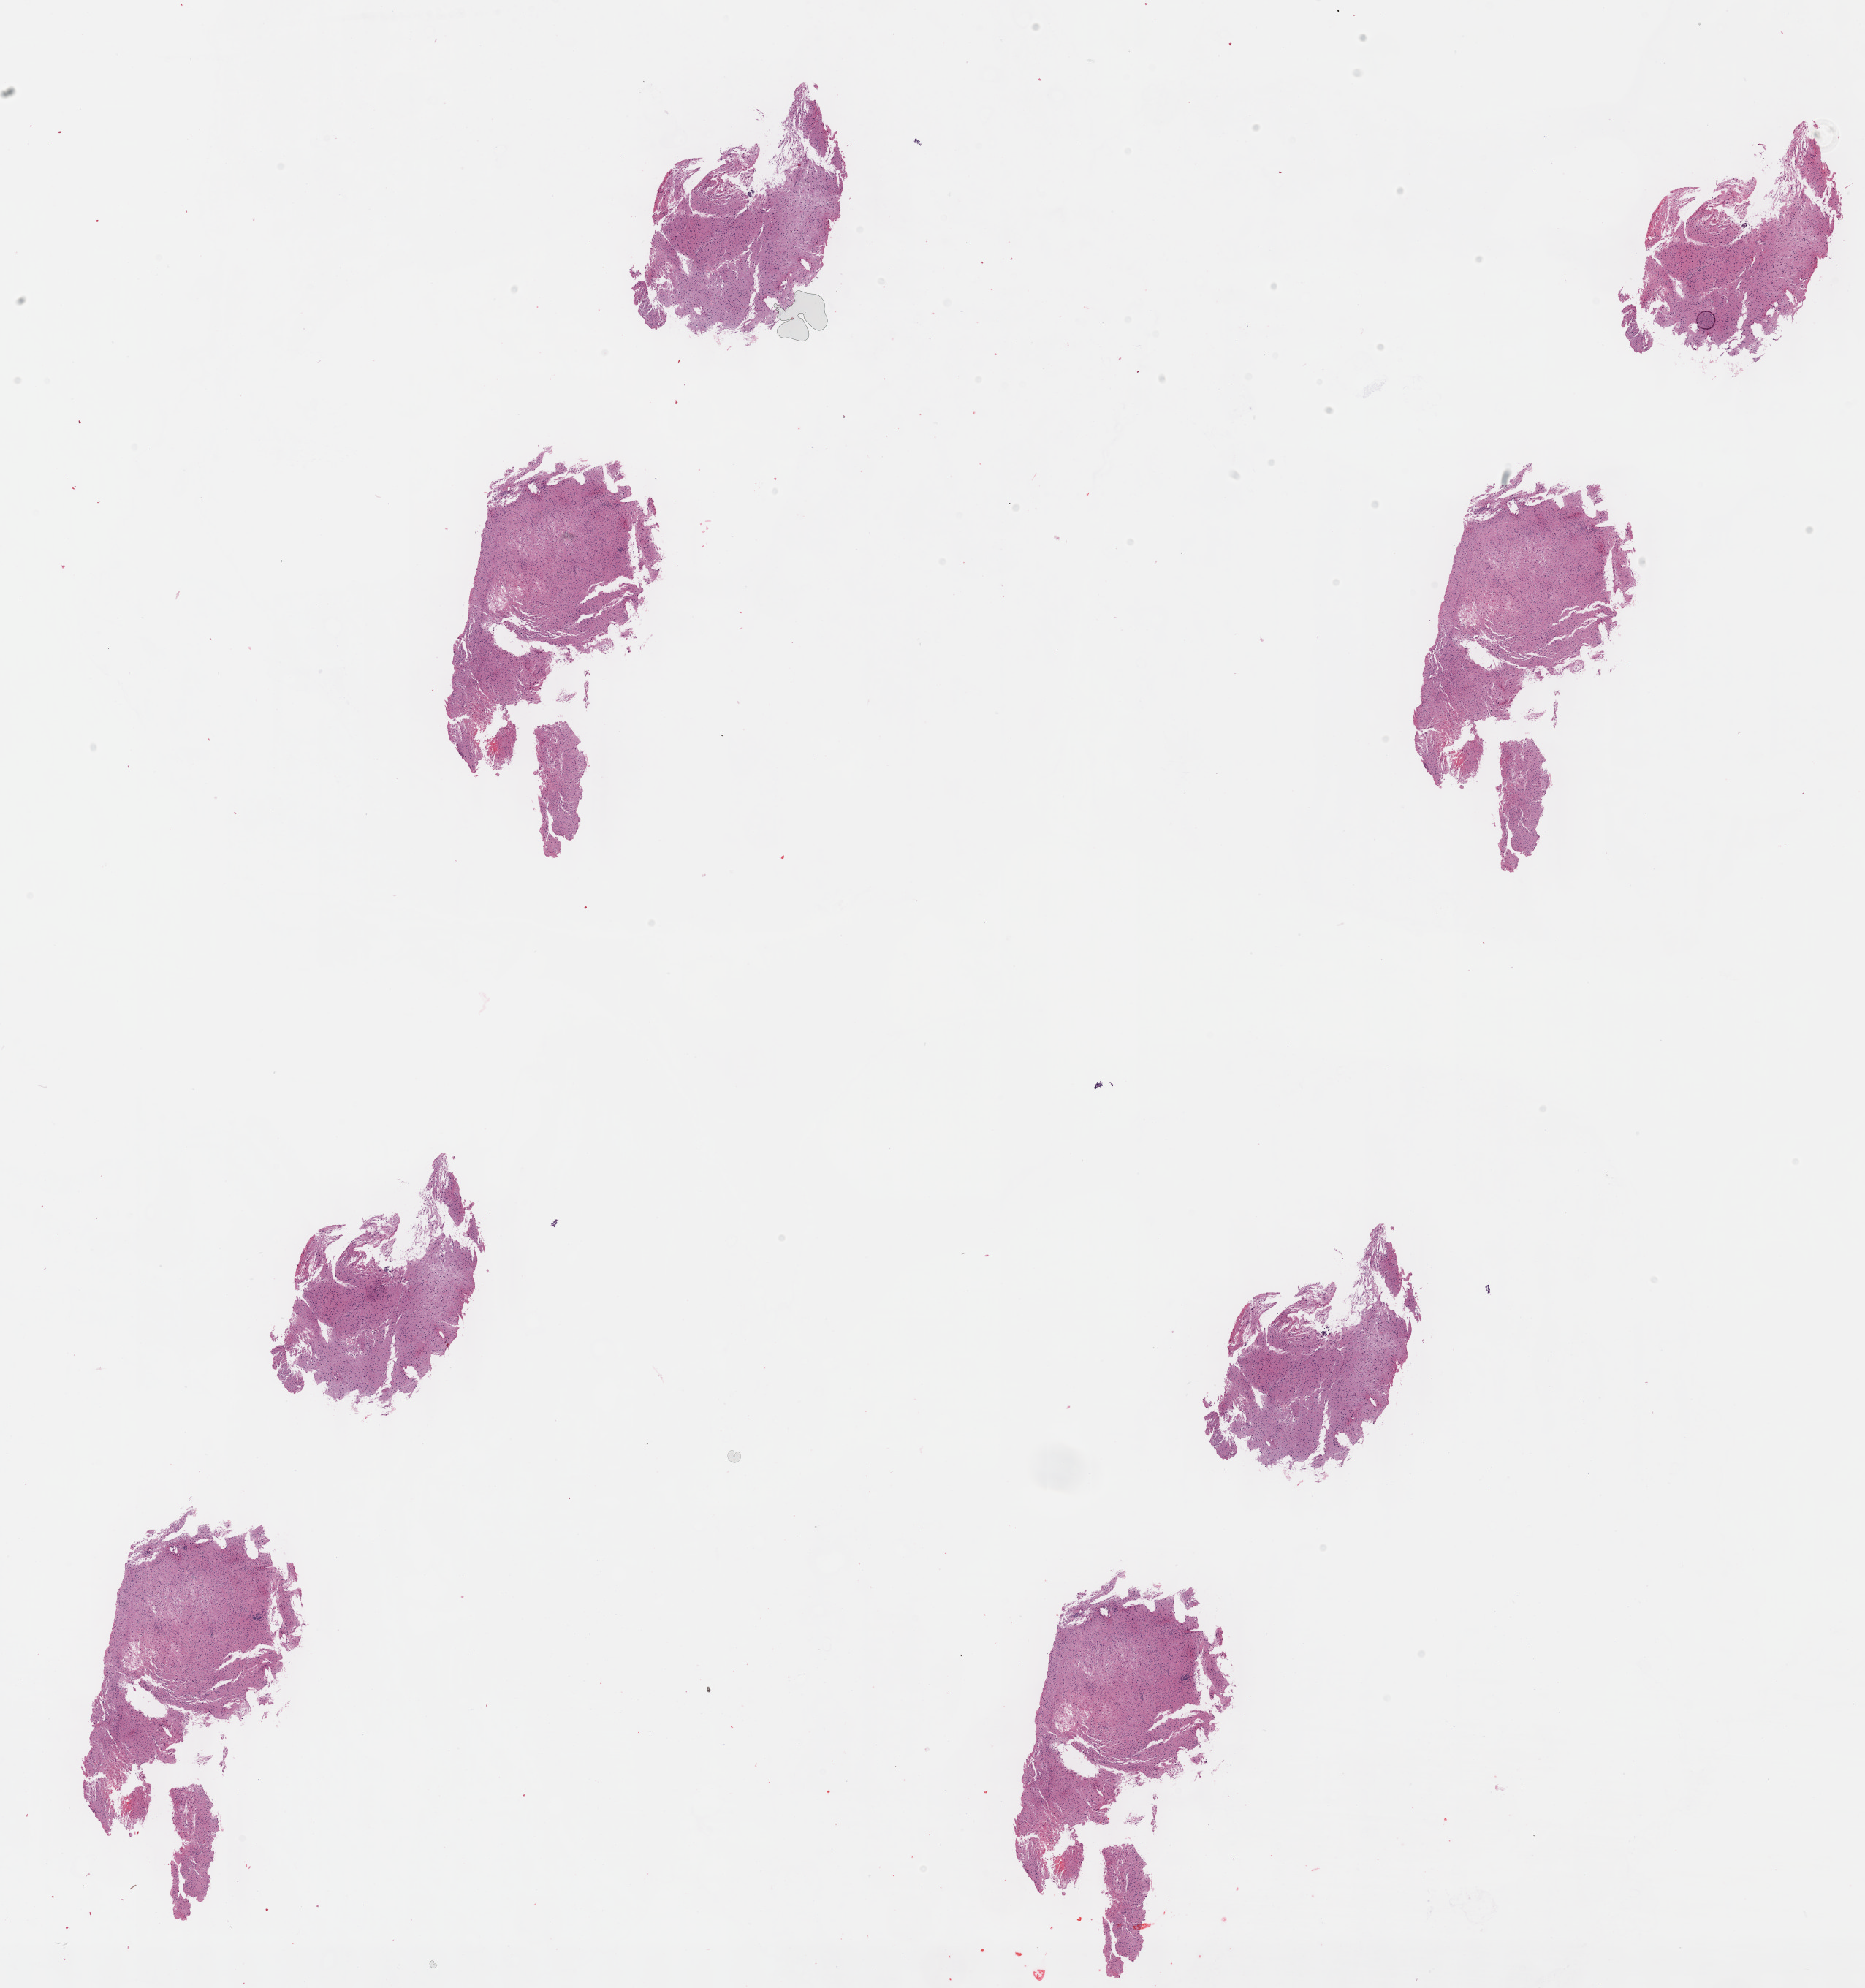
H&E whole-slide image — shown as a low-resolution overview of the whole scanned area (about 20.6 x 22.0 mm); formalin-fixed paraffin-embedded (FFPE) diagnostic section; primary tumour sample from the brain. Male patient; age at initial diagnosis 53 years. Histologic grade: G3 (poorly differentiated).
Pathologic diagnosis: Astrocytoma, anaplastic (cerebrum).